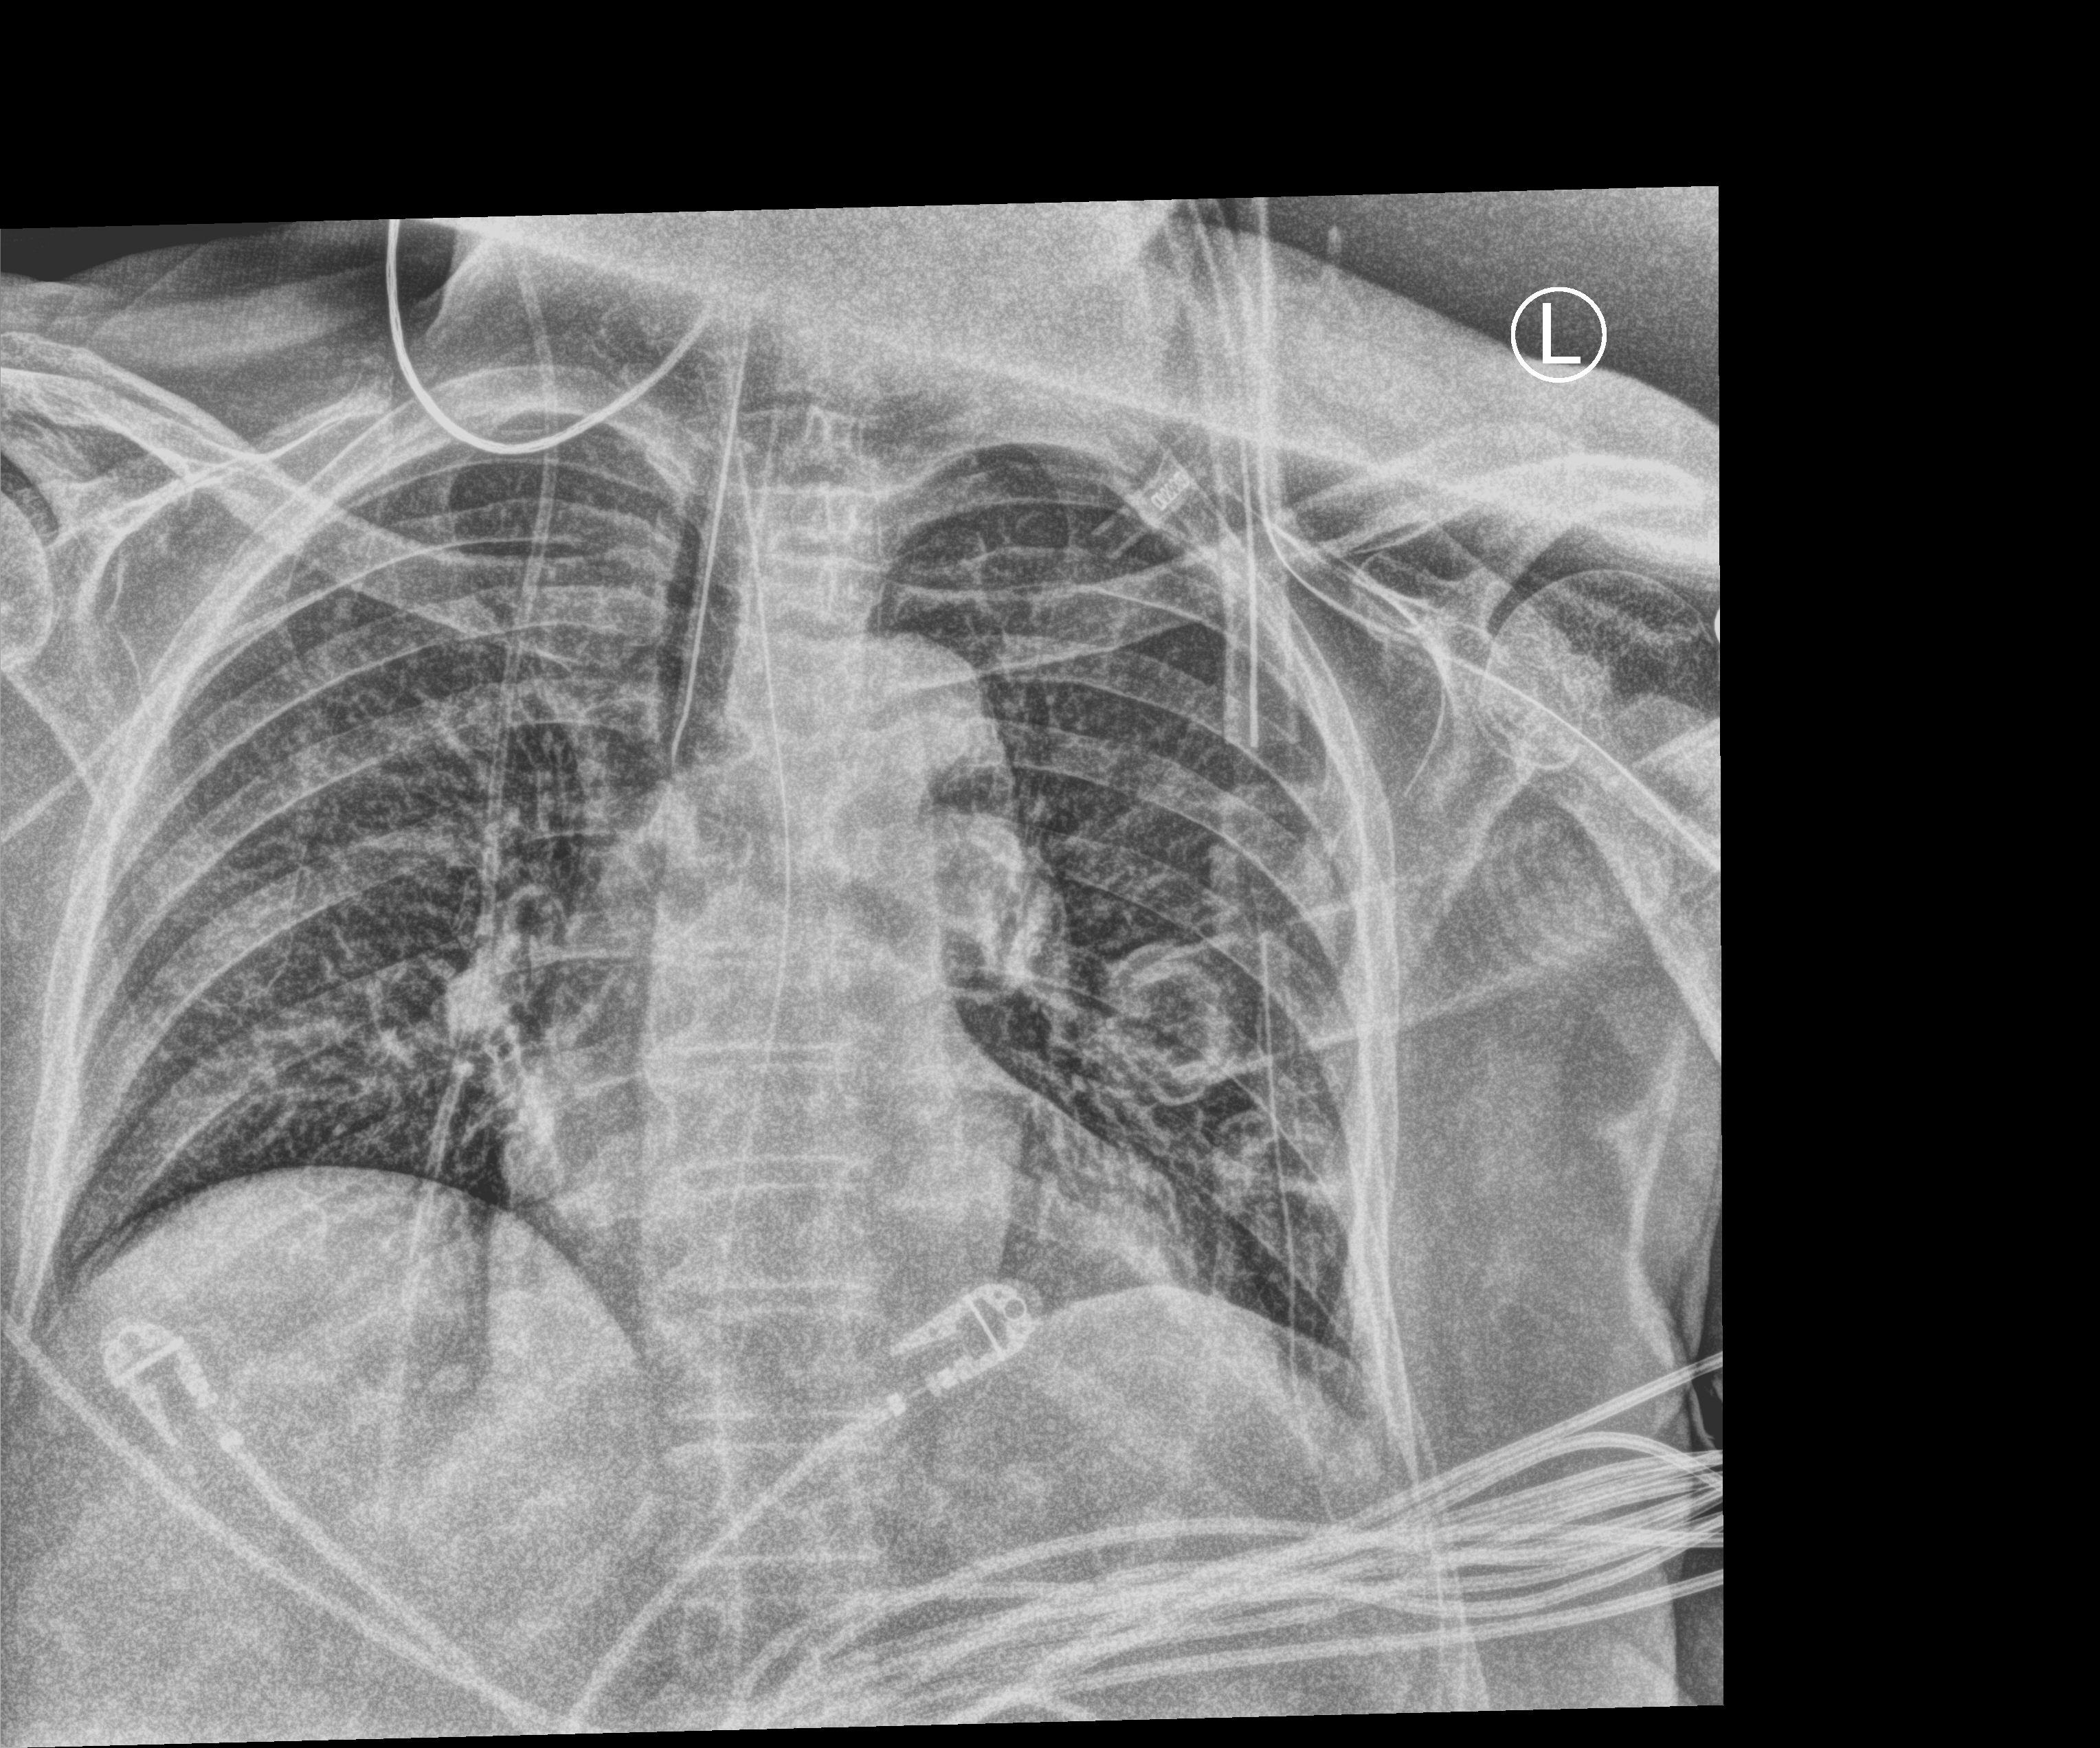
Portable chest radiograph; anteroposterior (AP) projection. Female patient hospitalised with COVID-19, age 75–90 years.
From the hospital-stay record, not from the radiograph (when in the stay this image was taken is not recorded): admitted to intensive care during this hospital stay: yes; mechanically ventilated during this hospital stay: yes.